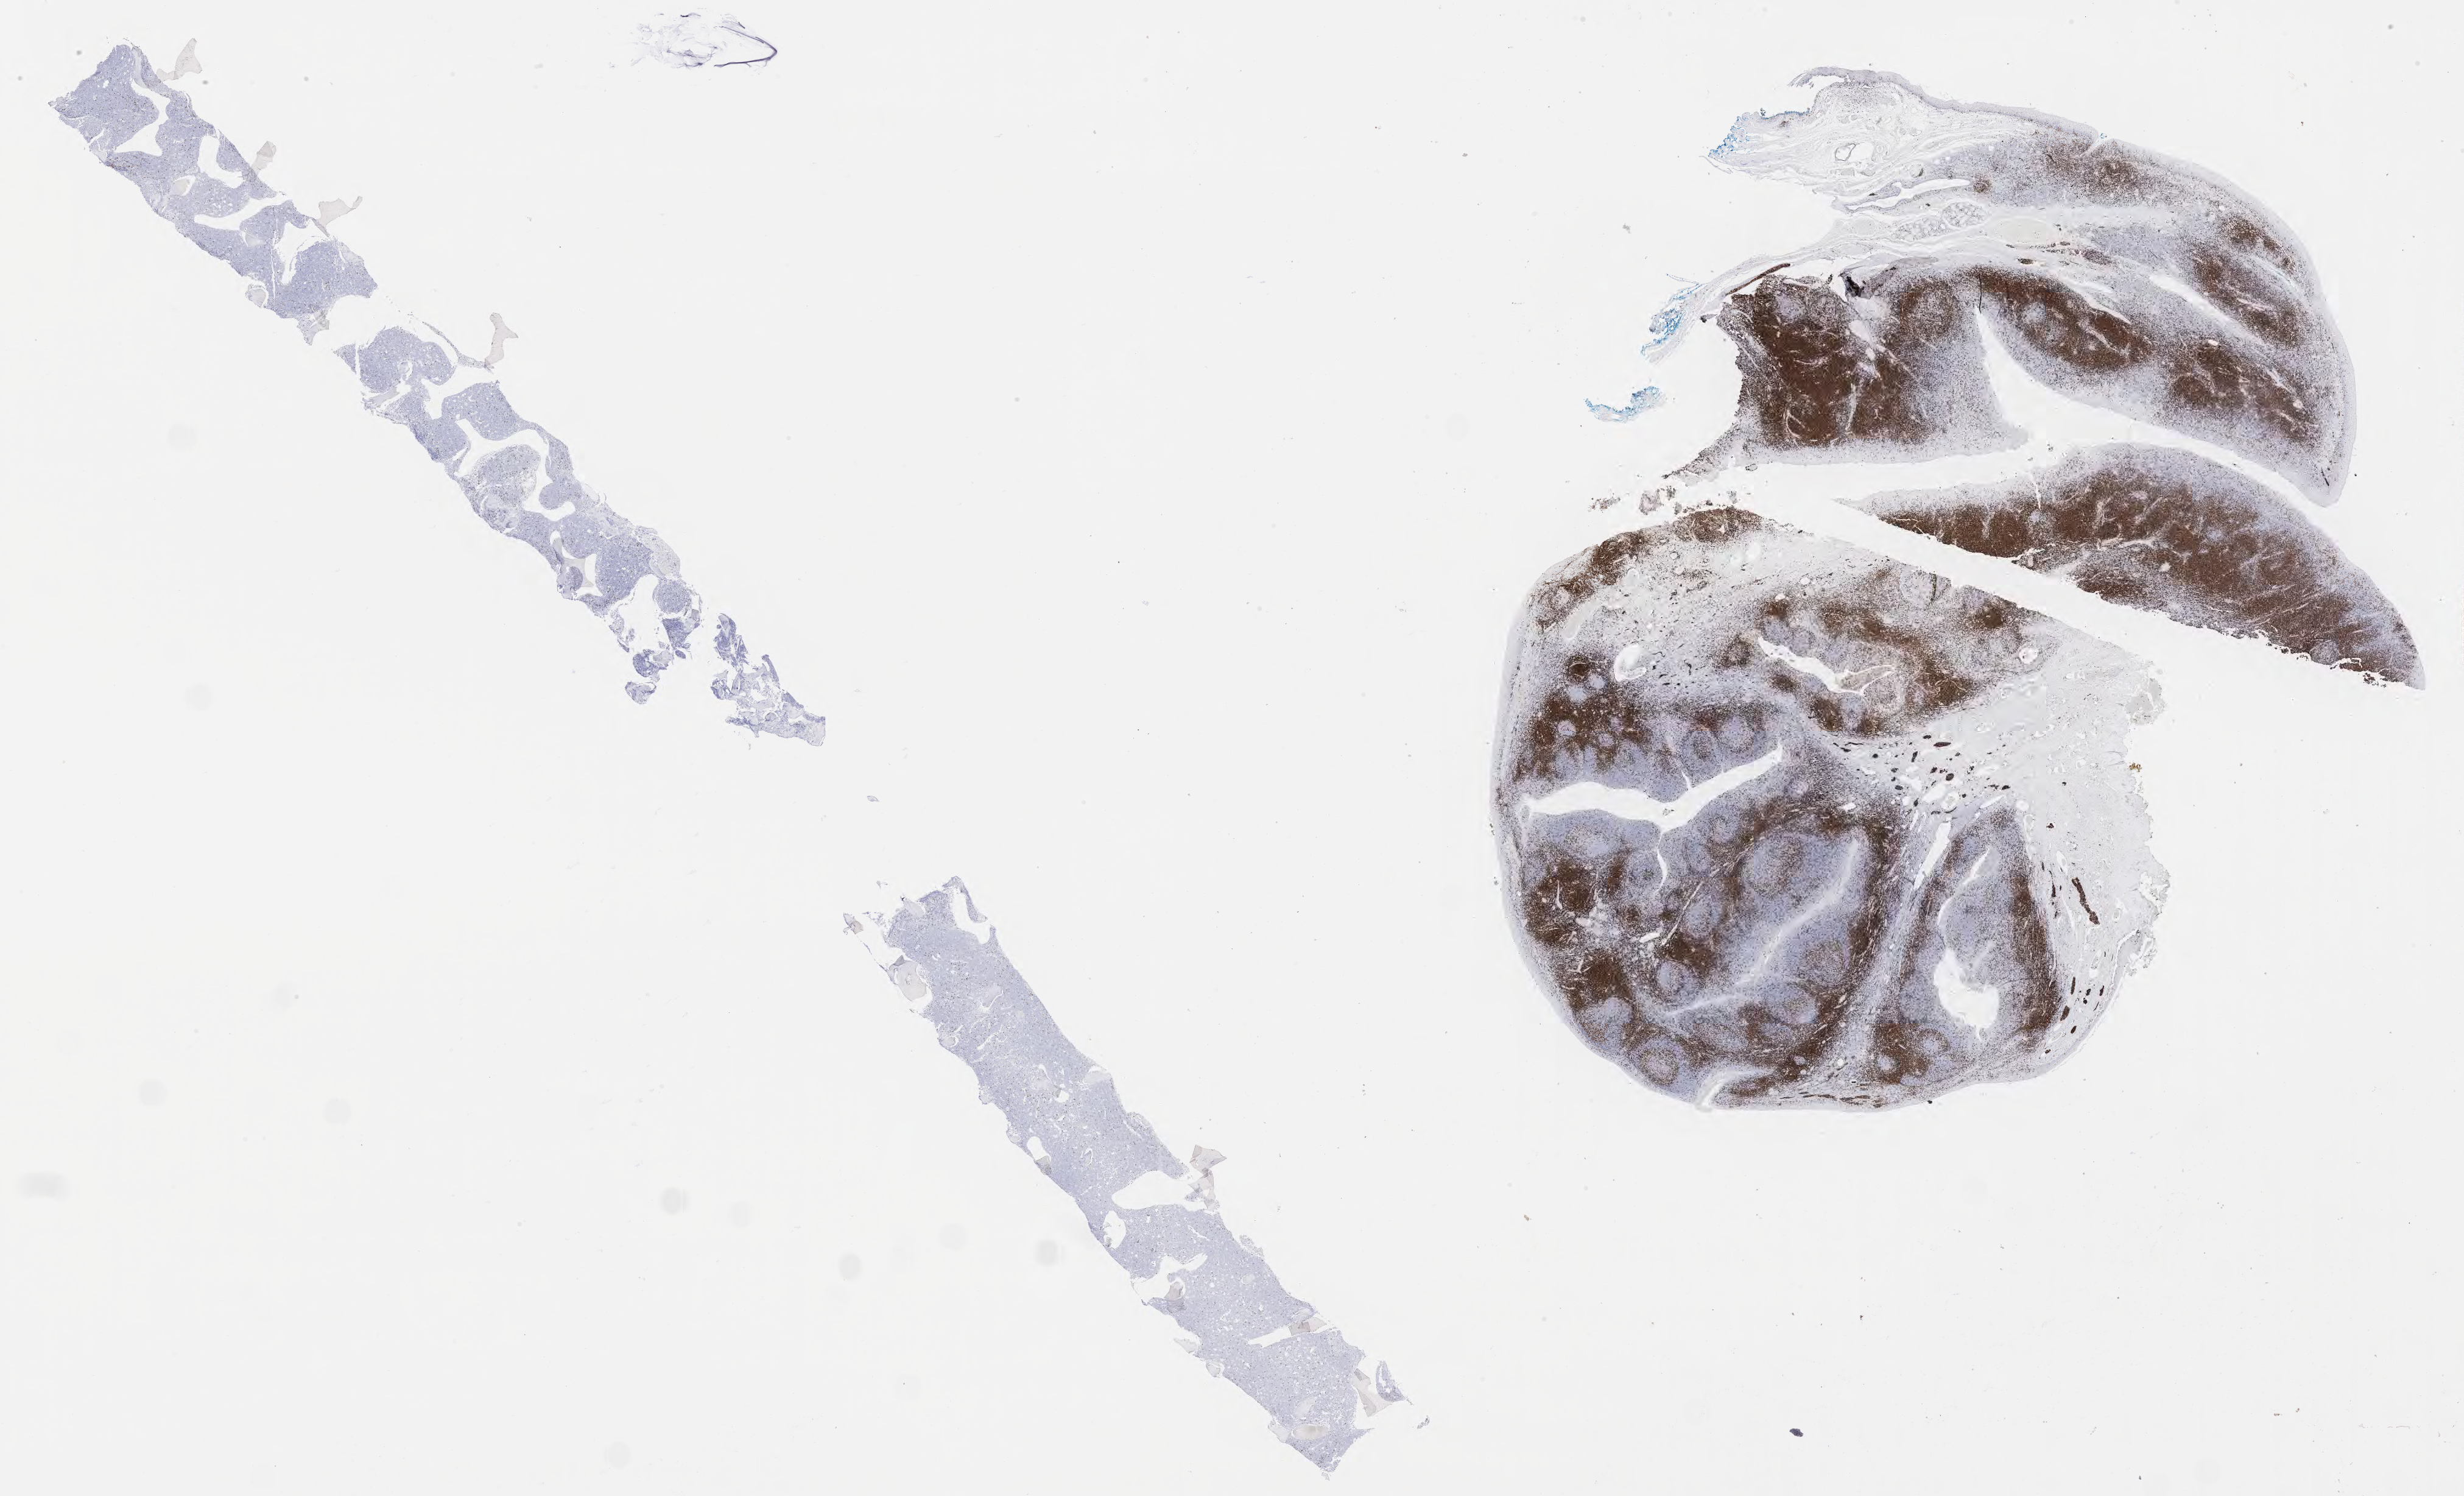
Immunohistochemistry (IHC) whole-slide image stained for CD3 — a low-resolution overview of the entire scanned area, about 32.7 x 19.9 mm. Tumor tissue. Patient: male, age at initial diagnosis 7 years.
Histologic diagnosis: Burkitt lymphoma, NOS.